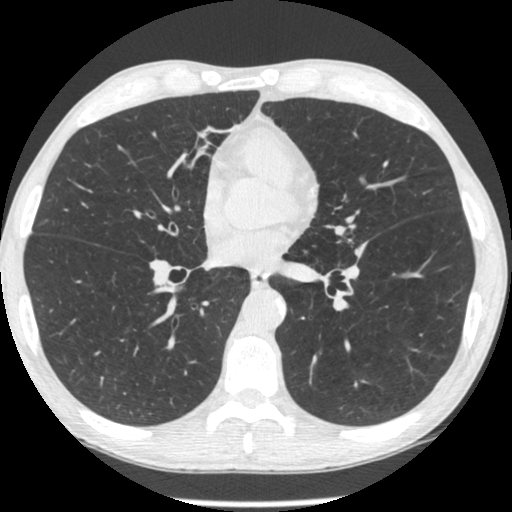
Low-dose screening chest CT, one axial slice. Position 129 of 293 along the scan axis. Reconstruction kernel STANDARD. Lung window (W 1500 / L -600 HU). 1.25 mm slice thickness. 512 × 512 image matrix.
Structures marked on this image (outlined manually by an expert reader):
- lesion 1 (tumor, upper lobe of left lung): bounding box [x1, y1, x2, y2] px = [356, 249, 362, 255]